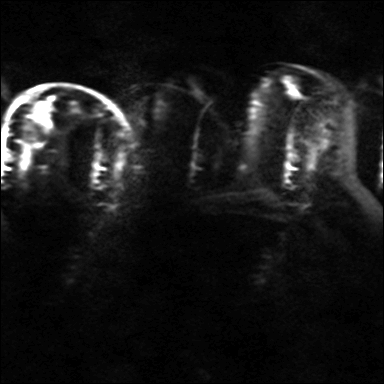
Breast MRI, one axial slice; slice 18 of 36 in the series (ordered by position); diffusion-weighted series; image 2 of 4 stored at this slice position (different b-values; order by instance number); 3 T; 4 mm slice thickness; 384 × 384 image matrix. Female patient.
Structures marked on this image (manually delineated by an expert):
- tumour on diffusion-weighted imaging: bounding box (x1, y1, x2, y2) in pixels: (23, 146, 32, 162)